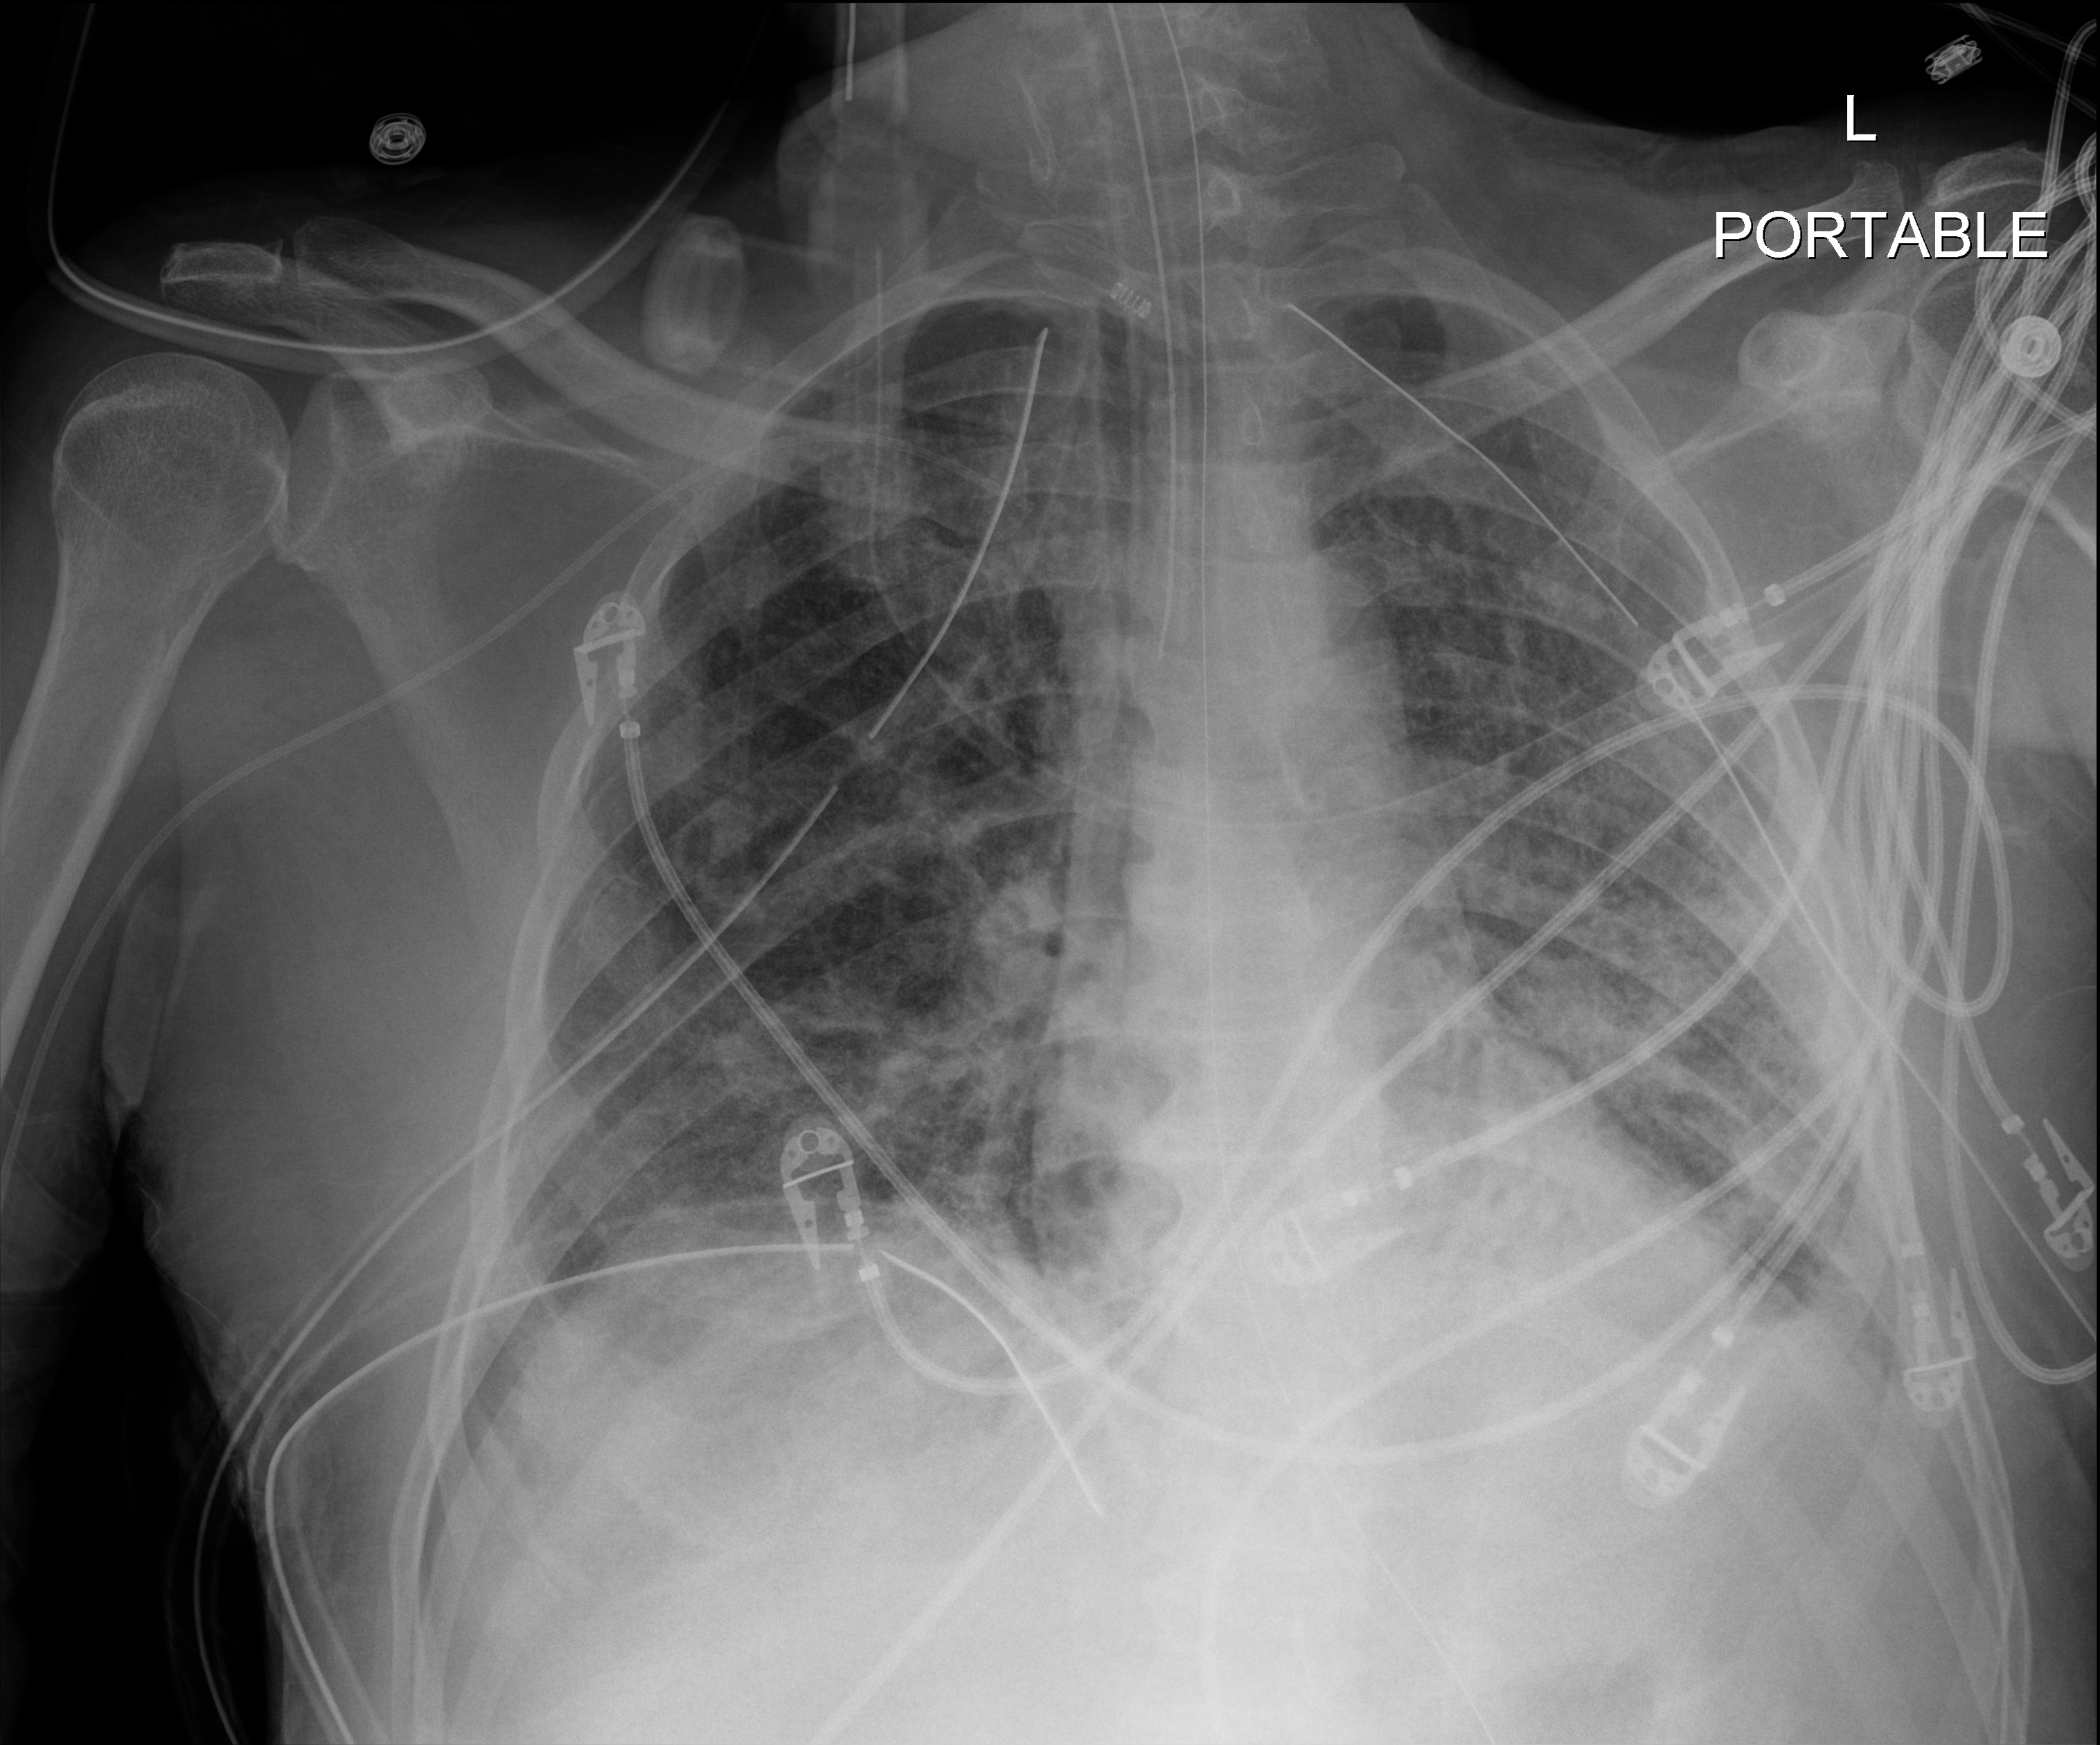
Bedside chest radiograph (digital radiography). Patient hospitalised with COVID-19; male, aged 18–59 years.
Admission-level facts for this patient (not findings on this image; timing relative to this image not recorded): length of hospital stay: 83 days; admitted to intensive care during this hospital stay: yes.